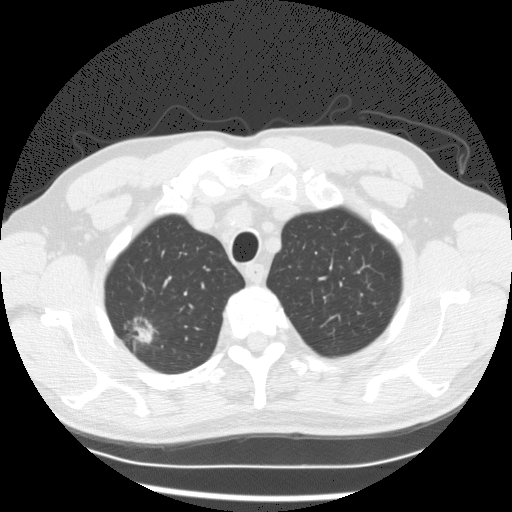
Low-dose screening chest CT, one axial slice; position 111 of 132 along the scan axis; 120 kVp; lung window (W 1500 / L -600 HU); 2.5 mm slice thickness; 512 × 512 image matrix, field of view 351 × 351 mm.
Outlined on this slice (outlined manually by an expert reader):
- lesion 1 (tumor, upper lobe of right lung): bounding box [x1, y1, x2, y2] px = [138, 329, 152, 344]